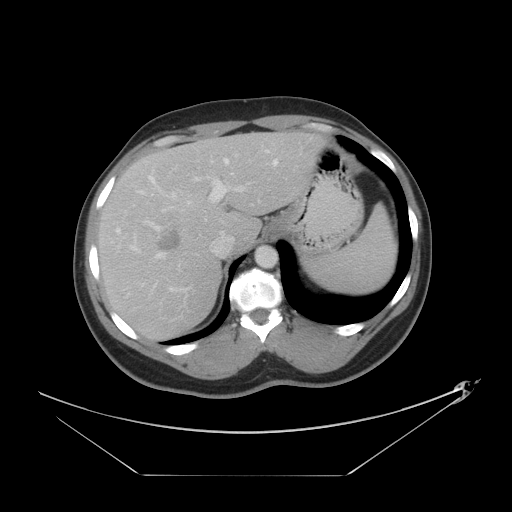
Contrast-enhanced abdominal CT, one axial slice. Slice 31 of 44 in the series (ordered by position). Reconstruction kernel STANDARD. 120 kVp. Intravenous contrast given. Soft-tissue window (W 400 / L 40 HU). 512 × 512 image matrix, field of view 466 × 466 mm. Male patient, age 49 years. From the clinical record (not read from this slice): diagnosis: colorectal cancer liver metastases, imaged before liver resection; multiple liver metastases: no; largest metastasis: 8.5 cm; chemotherapy before resection: yes.
Annotated regions visible in this slice (expert manual segmentation):
- hepatic veins: bounding box [x1, y1, x2, y2] px = [141, 158, 279, 258]
- liver: [98, 132, 325, 339]
- planned liver remnant (the part of the liver to remain after resection): [188, 132, 325, 249]
- portal vein (with intrahepatic branches): [116, 160, 246, 291]
- liver metastasis: [159, 227, 181, 251]